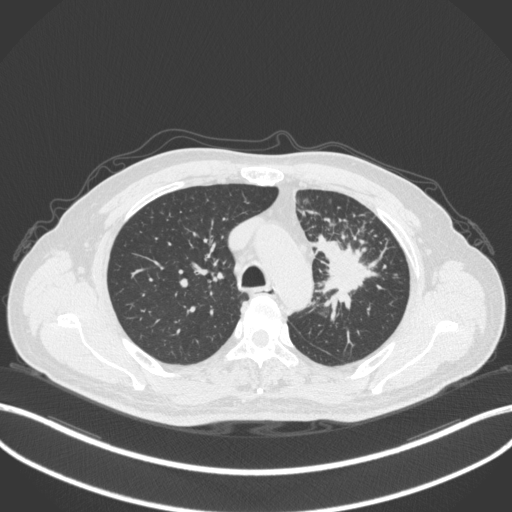
Chest CT, one axial slice. Slice 263 of 386 in the series (ordered by position). Reconstruction kernel B31f. 120 kVp. Lung window (W 1500 / L -600 HU). 1 mm slice thickness. 512 × 512 image matrix, field of view 400 × 400 mm. Male patient, age 69 years. From the clinical record (not read from this slice): clinical TNM (as recorded): T2a N2 M0; histopathological grade: G2-3.
Annotated regions visible in this slice (rectangle marked by the reading radiologist):
- lung tumour (recorded histology: adenocarcinoma): bounding box [x1, y1, x2, y2] px = [311, 233, 383, 311]